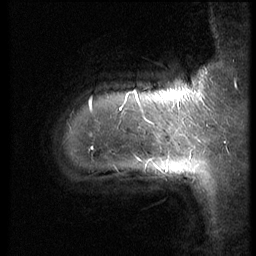
Breast MRI (dynamic contrast-enhanced), one sagittal slice; 3 images stored at this slice position (order not interpretable as contrast timing); 1.5 T; TE 4.2 ms, TR 9 ms; 256 × 256 image matrix. Patient: female, 39 years. Case-level facts recorded for this patient, not image findings: setting: breast cancer imaged before/during neoadjuvant chemotherapy; receptor status: HER2-positive.
Structures marked on this image (semi-automatic segmentation, software-assisted and operator-edited):
- analysis volume of interest (the breast-tissue region the enhancement analysis was run in; not a lesion): bounding box <42,64,171,212> (left, top, right, bottom; pixels)
- tumour enhancement mask (voxels above the 140 % enhancement threshold inside the analysis volume of interest): <91,91,136,148>